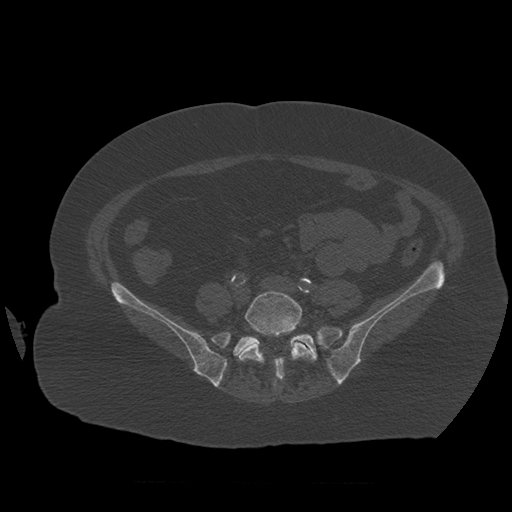
CT including the spine, one axial slice. Position 176 of 399 along the scan axis. Reconstruction kernel STANDARD. 120 kVp. Bone window (W 1800 / L 400 HU). 1.25 mm slice thickness. 512 × 512 image matrix, field of view 404 × 404 mm. Patient age 81 years. Case-level facts recorded for this patient, not image findings: primary cancer: renal.
Outlined on this slice (semi-automatic segmentation, software-assisted and operator-edited):
- L5 vertebra: bounding box [x1, y1, x2, y2] px = [239, 291, 312, 380]